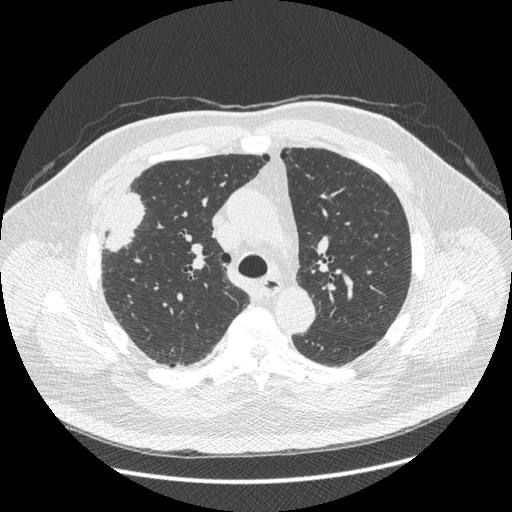
Low-dose screening chest CT, axial slice. Third annual screen. Lung window (W 1500 / L -600 HU). 1.25 mm slice thickness. 512 × 512 image matrix, field of view 400 × 400 mm. Male, age 66 years at enrolment. Current smoker at enrolment.
Lesion marked by an expert reader, bounding box (x1, y1, x2, y2) in pixels: (87, 194, 146, 268). Screening reader's record for this exam (one nodule recorded; not confirmed to be the boxed lesion): non-calcified nodule or mass ≥4 mm, right upper lobe, 48 × 25 mm, spiculated (stellate) margins, soft tissue attenuation, pre-existing on the prior screen: no. Official screen result: positive, other. Later outcome: lung cancer diagnosed 35 days after this screen — non-small cell carcinoma, right upper lobe, stage IV (AJCC 6th edition), 50 mm at pathology.